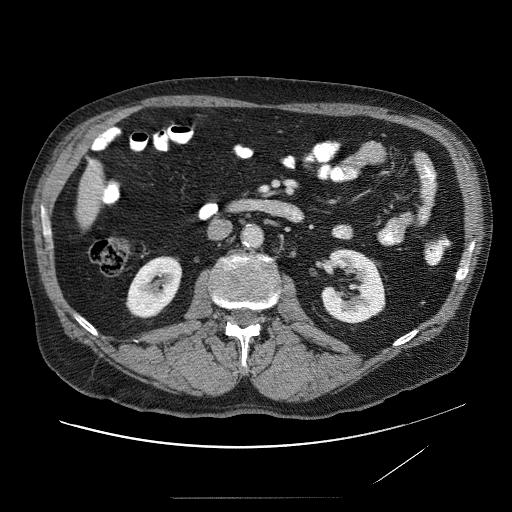
Contrast-enhanced abdominal CT (liver protocol), one axial slice; position 7 of 89 along the scan axis; reconstruction kernel STANDARD; soft-tissue window (W 400 / L 40 HU); 2.5 mm slice thickness; 512 × 512 image matrix, field of view 420 × 420 mm. From the clinical record (not read from this slice): diagnosis: hepatocellular carcinoma (patient treated with transarterial chemoembolisation; whether this scan precedes or follows treatment is not stated here); TNM stage (as recorded): Stage-IVA.
Outlined on this slice (semi-automatic segmentation, software-assisted and operator-edited):
- liver parenchyma outside the tumour (the mass and vessels are separate outlines, so this box may not span the whole liver): bounding box [x1, y1, x2, y2] px = [92, 152, 98, 156]